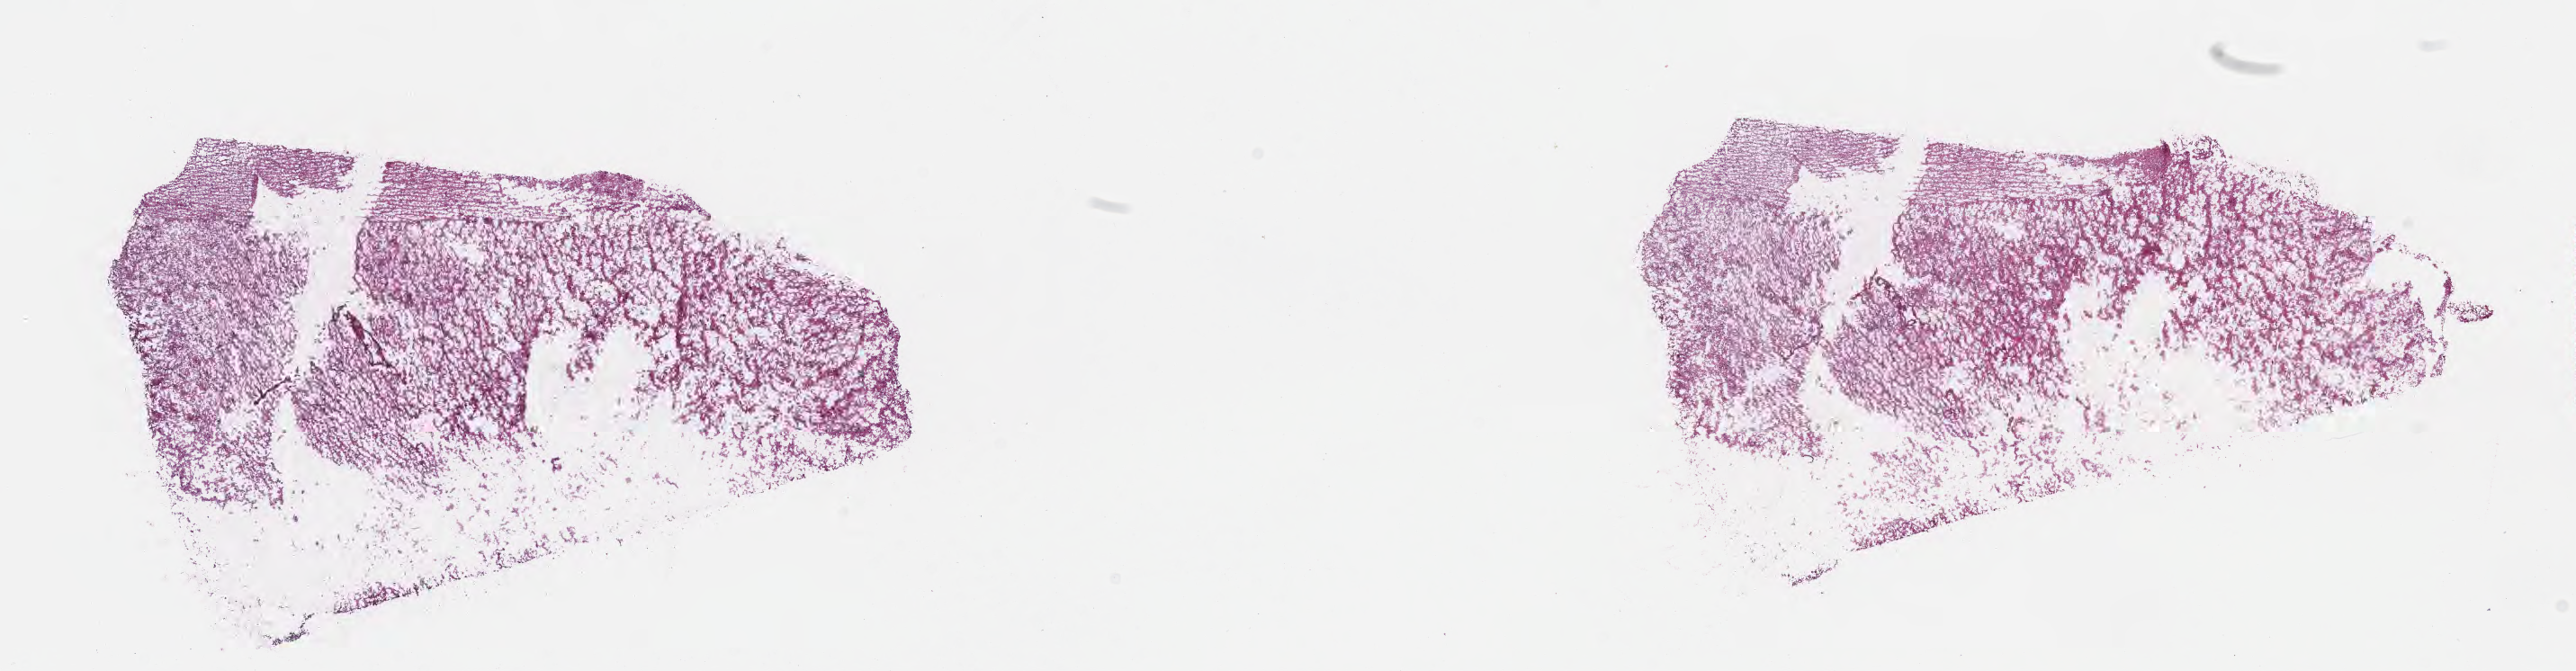
Digitized haematoxylin and eosin-stained section — whole scanned area (about 23.1 x 6.0 mm) shown as a low-resolution overview, frozen section, recurrent tumor, site: brain. Female, age 59 years at initial diagnosis. Pathologist review of this section (percent, as recorded): tumor cells 78%, tumor nuclei 90%.
Patient diagnosis: Glioblastoma, NOS.